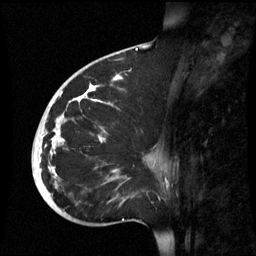
Breast MRI (dynamic contrast-enhanced), one sagittal slice. Position 32 of 60 along the scan axis. Dynamic contrast-enhanced series, image 2 of 3 at this slice position (ordered by acquisition). 1.5 T. TE 4.2 ms, TR 8.9 ms. 2.6 mm slice thickness. 256 × 256 image matrix. Female patient, age 35 years. Case-level facts recorded for this patient, not image findings: setting: breast cancer imaged before/during neoadjuvant chemotherapy; receptor status: HR-positive, HER2-negative.
Structures marked on this image (semi-automatic segmentation, software-assisted and operator-edited):
- analysis volume of interest (the breast-tissue region the enhancement analysis was run in; not a lesion): bounding box (x1, y1, x2, y2) in pixels: (32, 74, 164, 221)
- tumour enhancement mask (voxels above the 70 % enhancement threshold inside the analysis volume of interest): (39, 74, 122, 177)